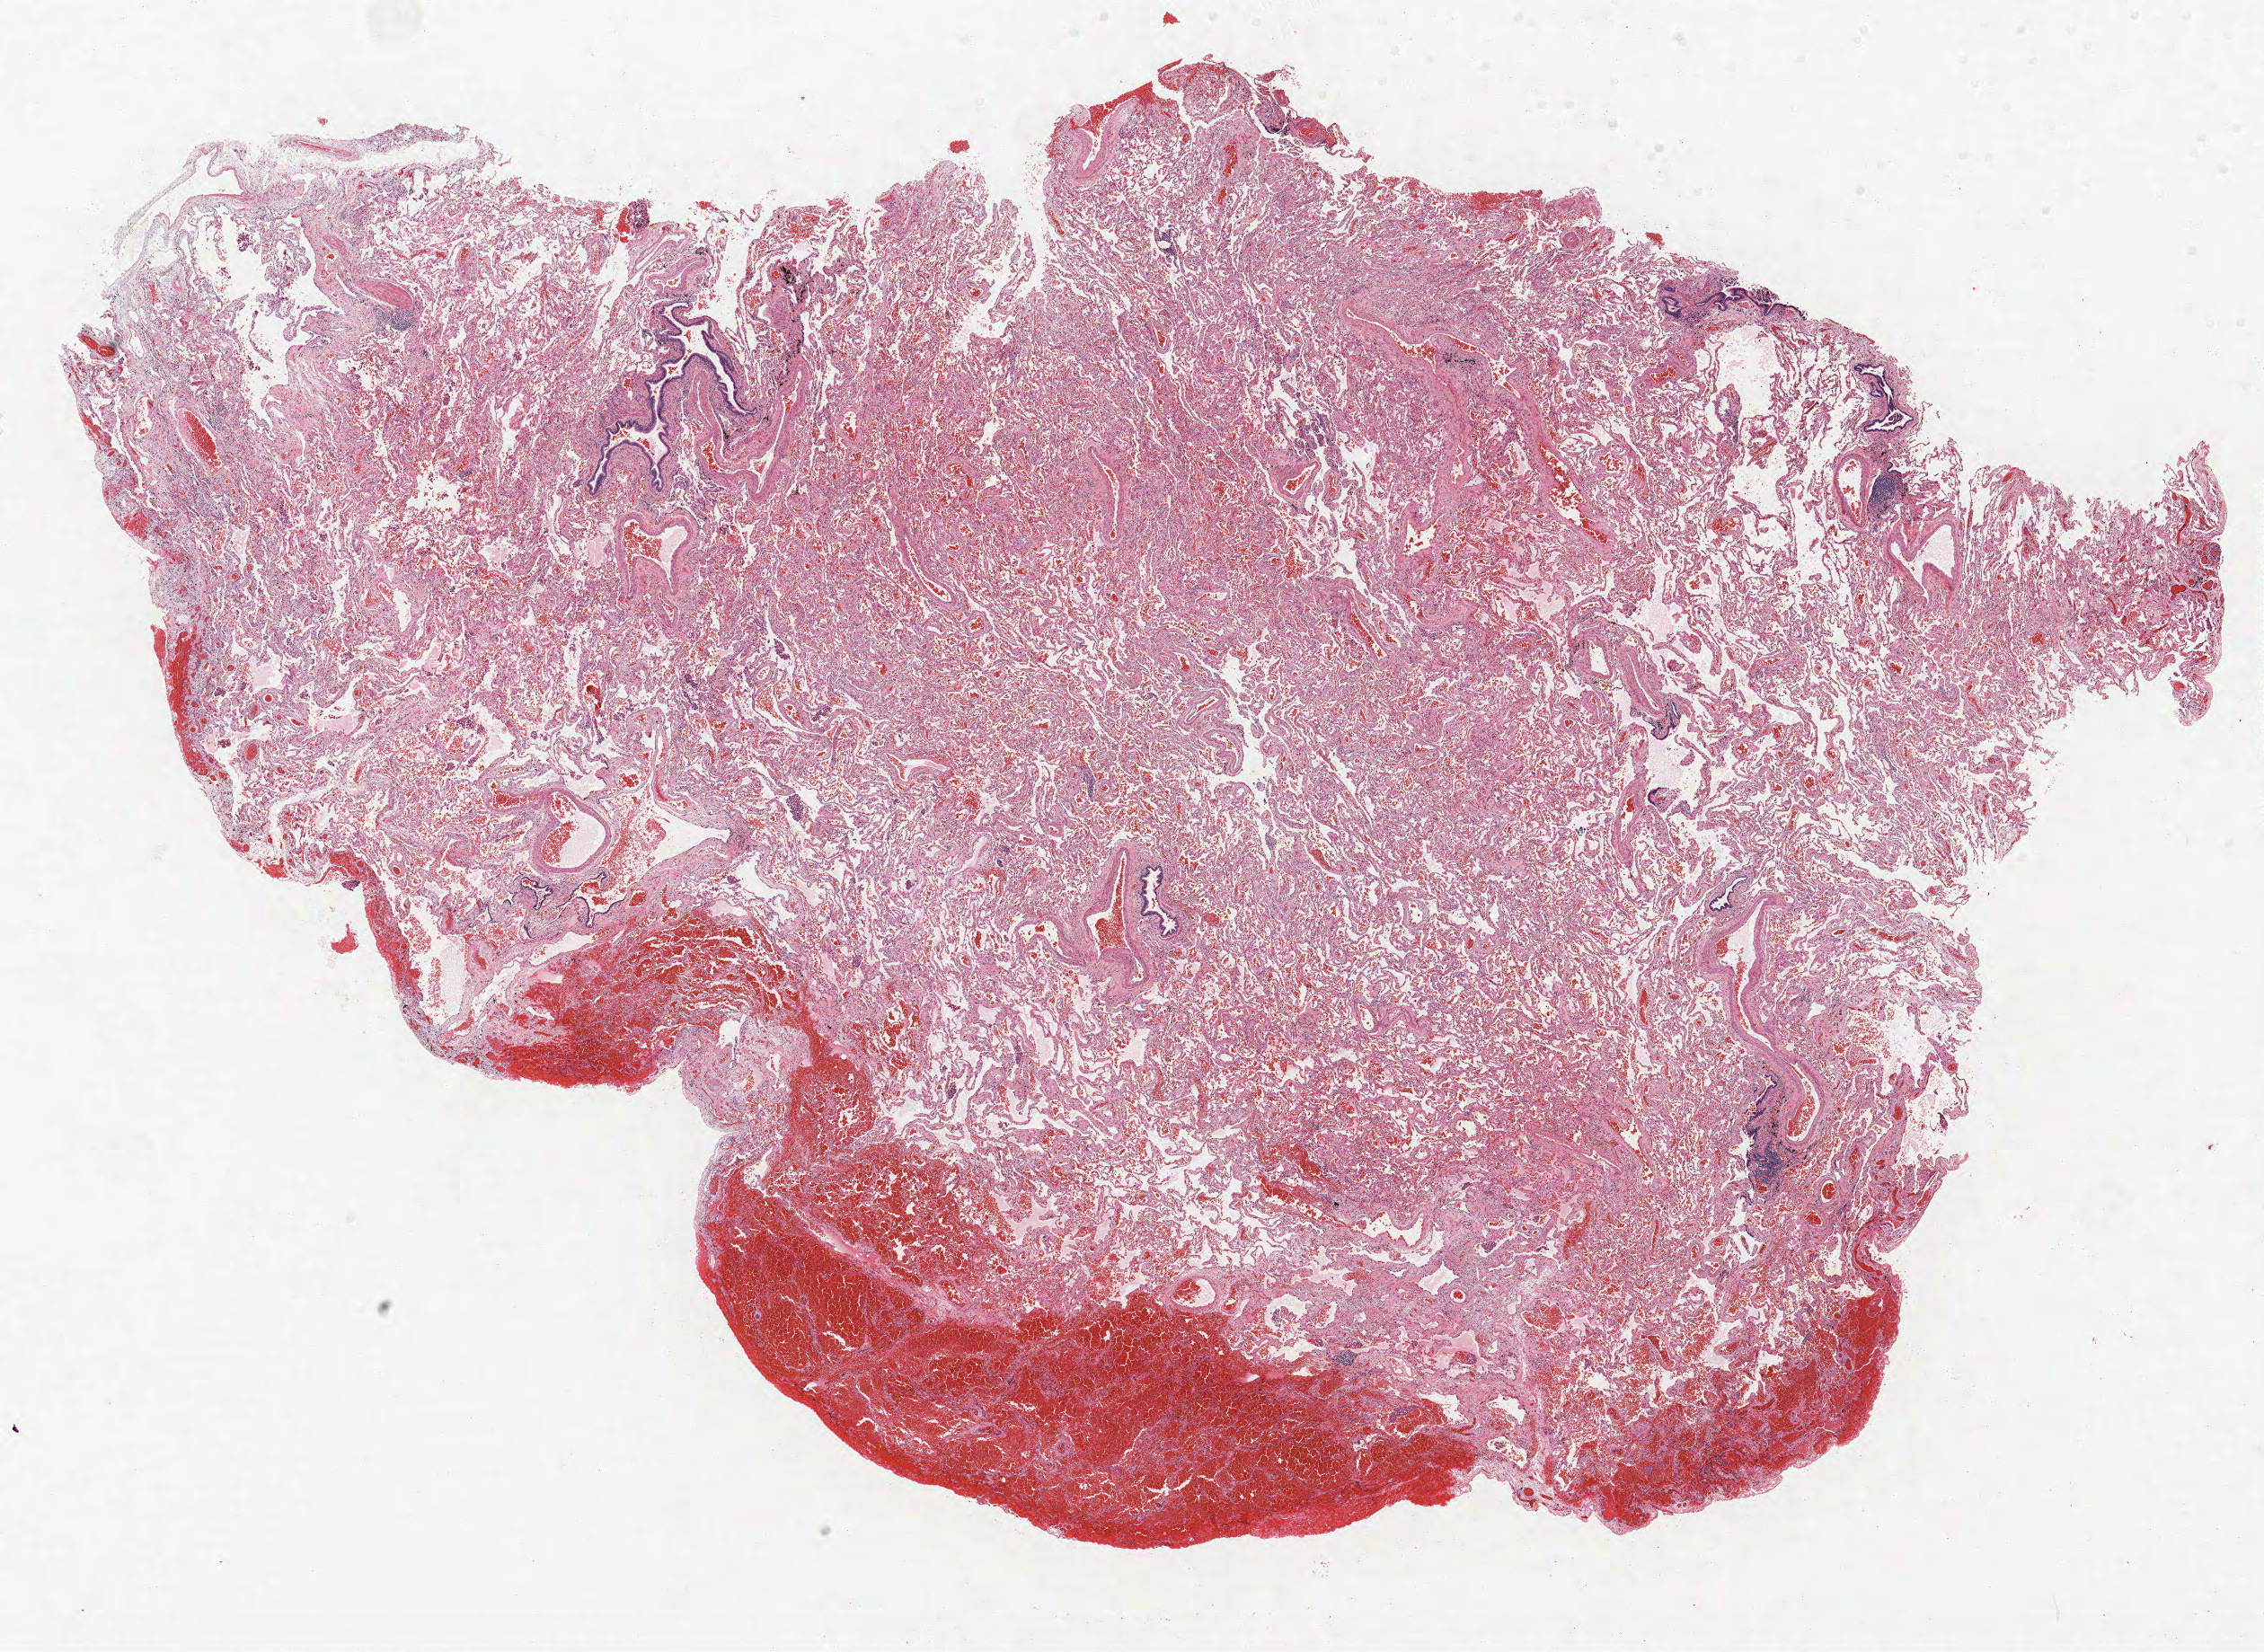
Whole-slide histology image, H&E, a low-resolution overview of the entire scanned area, about 20.2 x 14.7 mm (from a 40x scan), FFPE section, lung. Female, age 67 at enrolment. Grade: moderately differentiated (G2).
Participant's lung-cancer diagnosis: Adenocarcinoma, NOS. Stage (AJCC 6th edition): IA. ICD-O-3 topography: upper lobe of lung (C34.1). Primary tumour location (clinical record): right upper lobe. Tumour size (pathology): 14 mm.